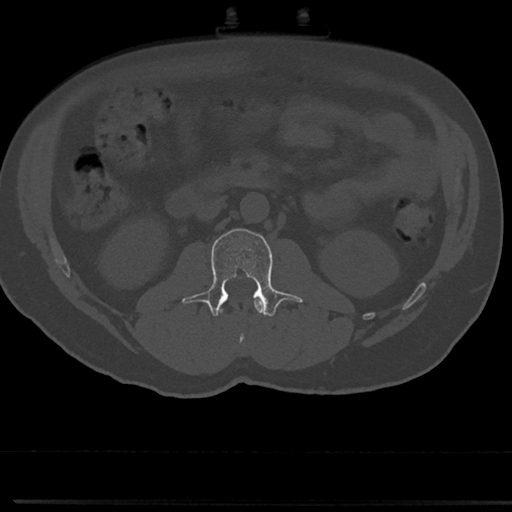
CT including the spine, one axial slice; slice 25 of 817 in the series (ordered by position); reconstruction kernel Br40s/3; 120 kVp; bone window (W 1800 / L 400 HU); 0.5 mm slice thickness; 512 × 512 image matrix. Patient: male, 61 years. From the clinical record (not read from this slice): primary cancer: prostate.
Structures marked on this image (semi-automatic segmentation, software-assisted and operator-edited):
- L1 vertebra: bounding box [x1, y1, x2, y2] px = [219, 298, 263, 349]
- L2 vertebra: [191, 228, 300, 318]